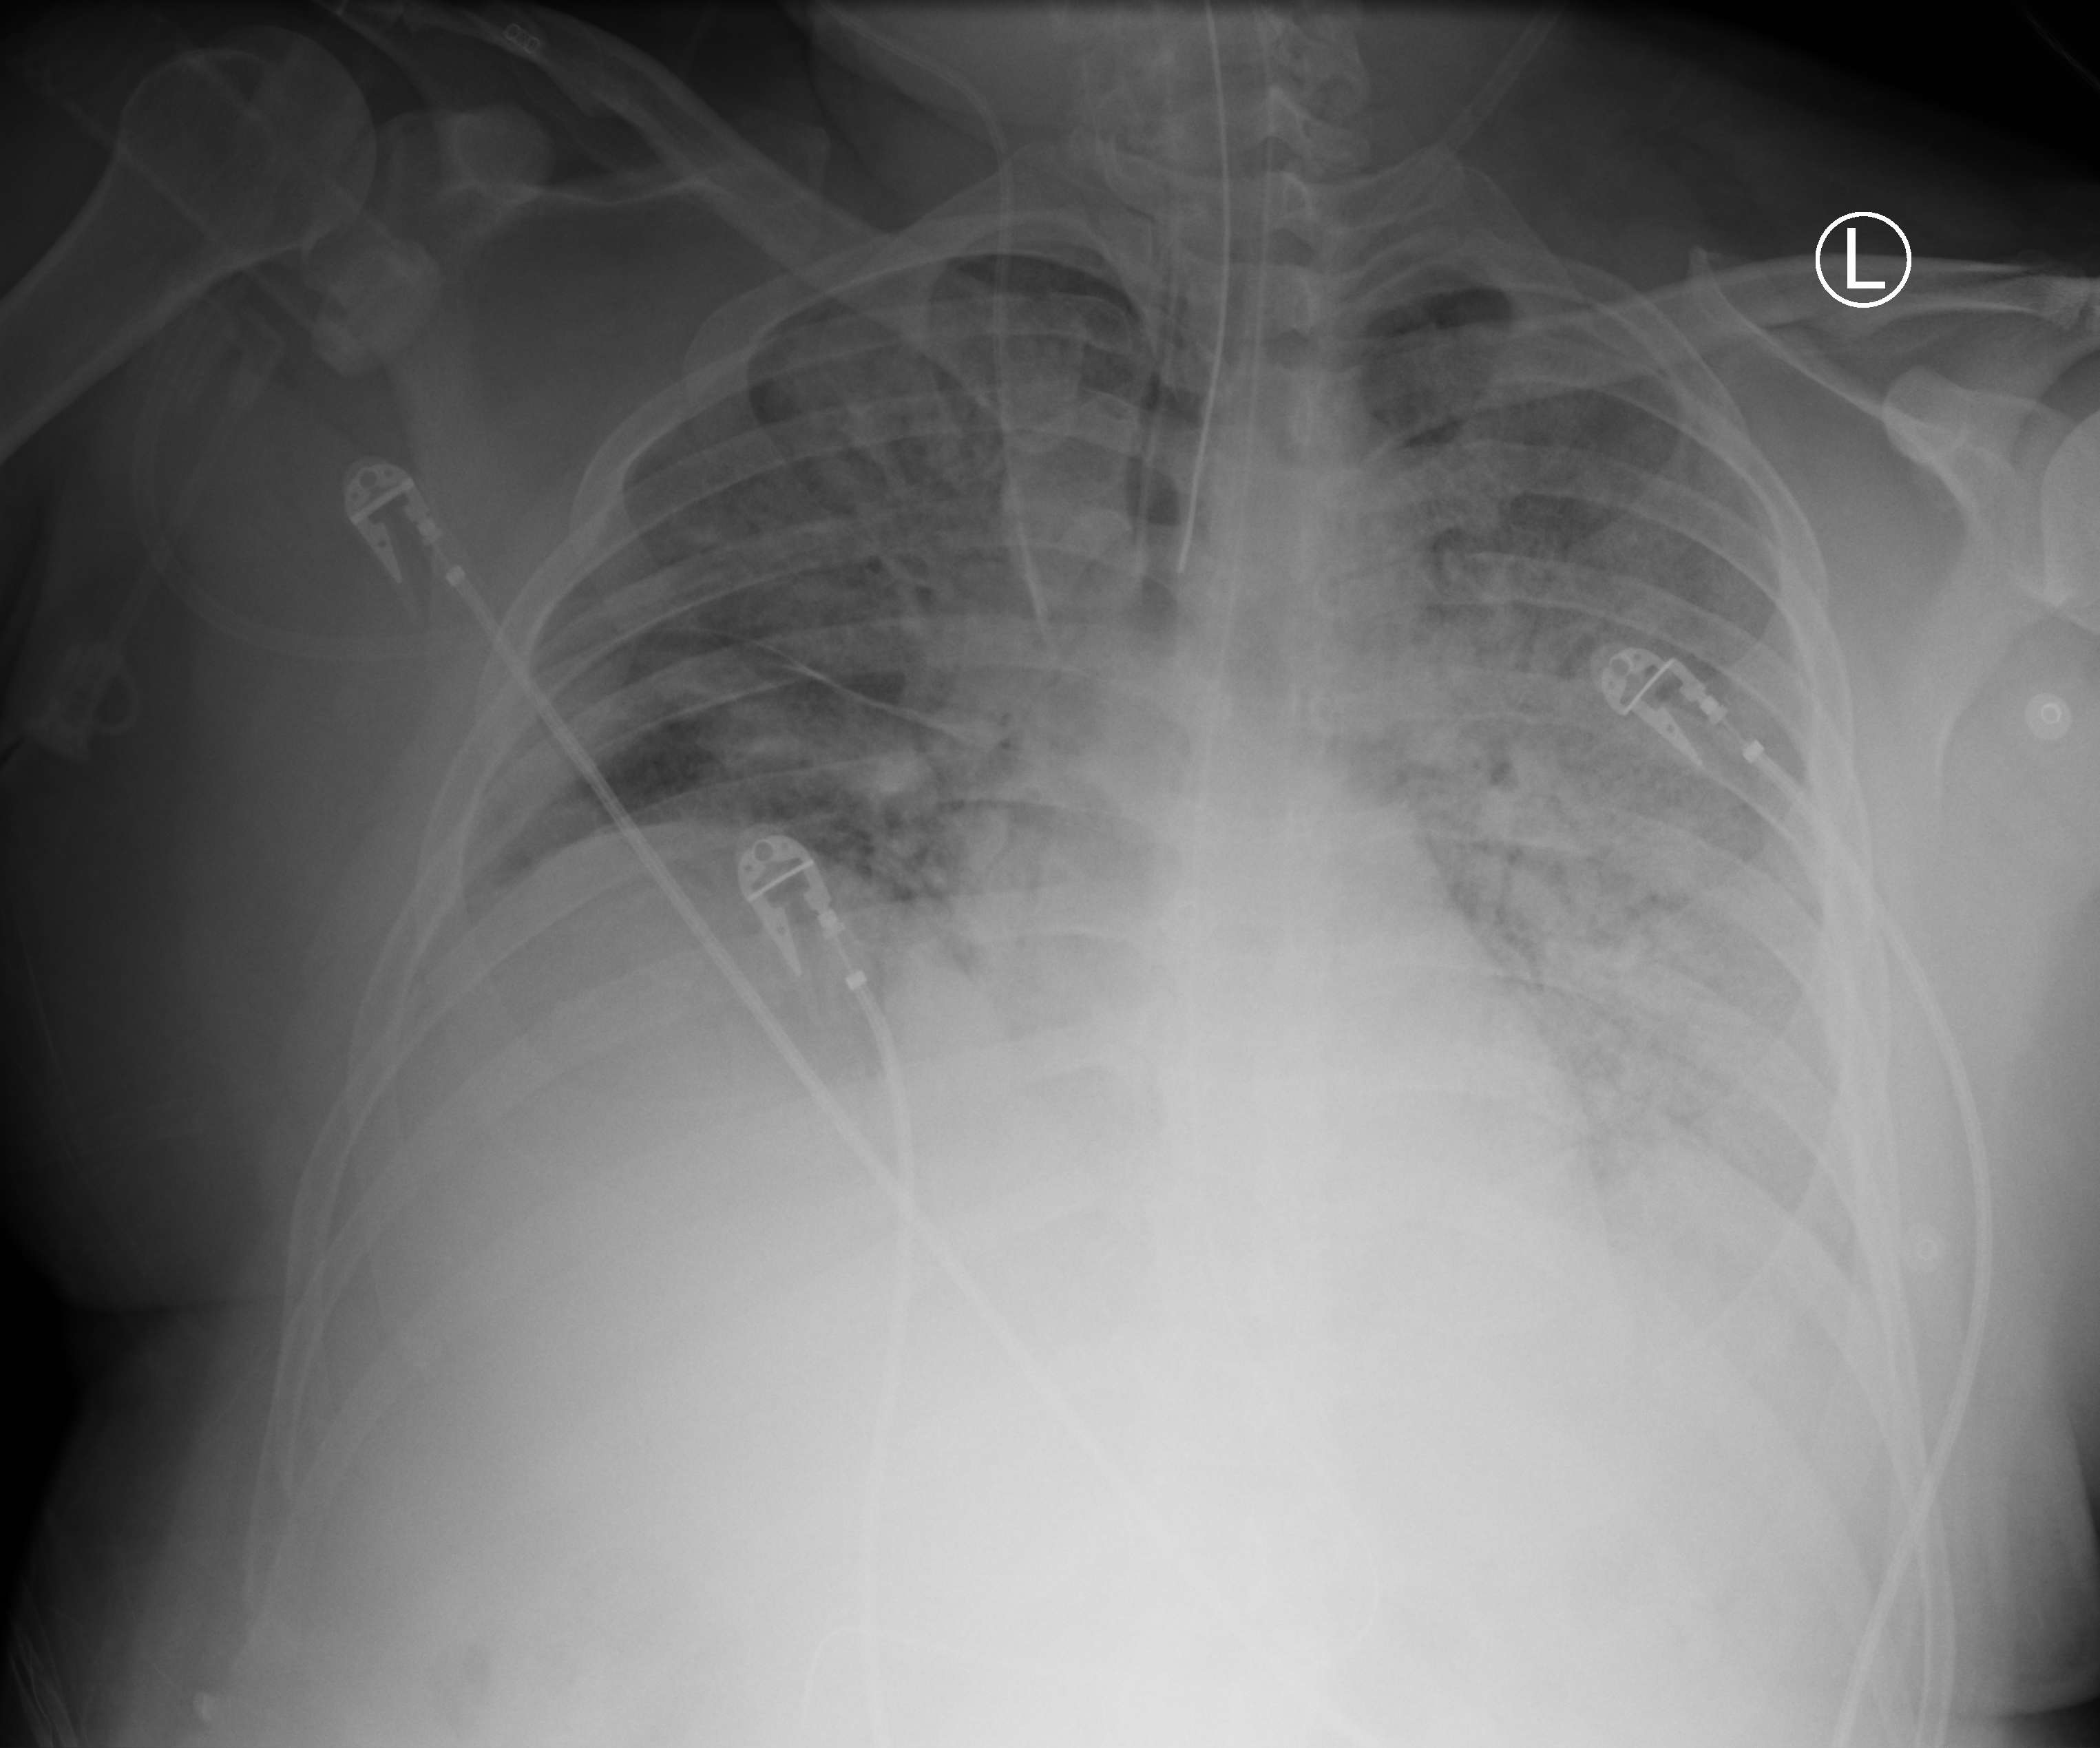
Bedside chest radiograph (computed radiography), anteroposterior (AP) projection. Patient hospitalised with COVID-19; male, aged 18–59 years.
Admission-level facts for this patient (not findings on this image; timing relative to this image not recorded): admitted to intensive care during this hospital stay: yes; mechanically ventilated during this hospital stay: yes.